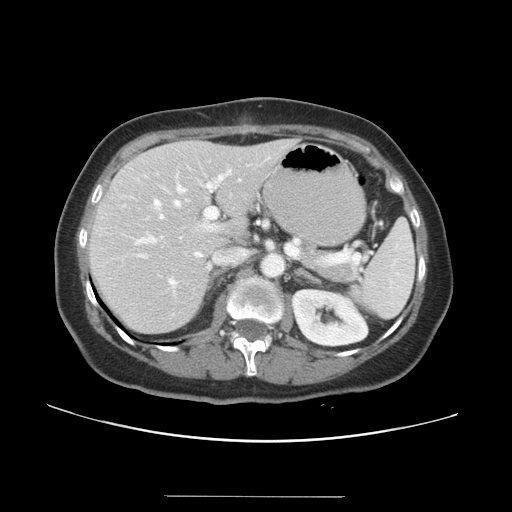
Contrast-enhanced abdominal CT, one axial slice; slice 21 of 34 in the series (ordered by position); reconstruction kernel STANDARD; 120 kVp; intravenous contrast given; soft-tissue window (W 400 / L 40 HU); 5 mm slice thickness; 512 × 512 image matrix, field of view 382 × 382 mm. Female patient, age 69 years. Case-level facts recorded for this patient, not image findings: diagnosis: colorectal cancer liver metastases, imaged before liver resection; multiple liver metastases: yes; largest metastasis: 1.4 cm; disease in both lobes: yes.
Annotated regions visible in this slice (outlined manually by an expert reader):
- hepatic veins: bounding box (x1, y1, x2, y2) in pixels: (147, 180, 245, 290)
- liver: (90, 140, 296, 333)
- planned liver remnant (the part of the liver to remain after resection): (90, 140, 296, 333)
- portal vein (with intrahepatic branches): (136, 171, 360, 264)